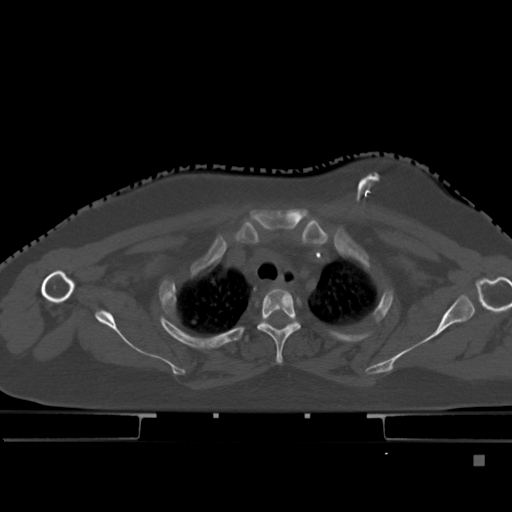
CT including the spine, one axial slice. Slice 357 of 495 in the series (ordered by position). Bone window (W 1800 / L 400 HU). 1.5 mm slice thickness. 512 × 512 image matrix, field of view 404 × 404 mm. Patient: female, 33 years. From the clinical record (not read from this slice): primary cancer: breast; vertebrae with lytic lesions (as recorded): T1.
Structures marked on this image (semi-automatic segmentation, software-assisted and operator-edited):
- T2 vertebra: bounding box [x1, y1, x2, y2] px = [257, 288, 301, 365]
- T3 vertebra: [245, 336, 248, 342]